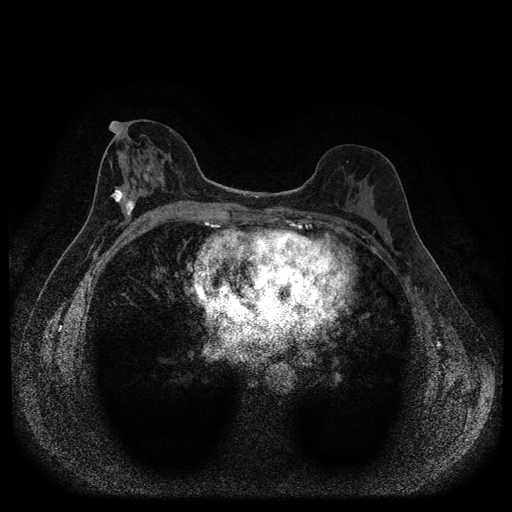
Breast MRI (dynamic contrast-enhanced, multi-phase), one axial slice. Position 50 of 116 along the scan axis. Dynamic contrast-enhanced series, time point 2 of 5 at this slice position (early post-contrast). 1.5 T. TE 2.7 ms, TR 5.4 ms. 512 × 512 image matrix. Patient: female, 49 years.
Annotated regions visible in this slice (semi-automatically segmented with operator editing):
- breast lesion (labelled 'tumour' in the annotation; benign lesions carry a separate 'benign' label): bounding box [x1, y1, x2, y2] px = [110, 187, 137, 224]